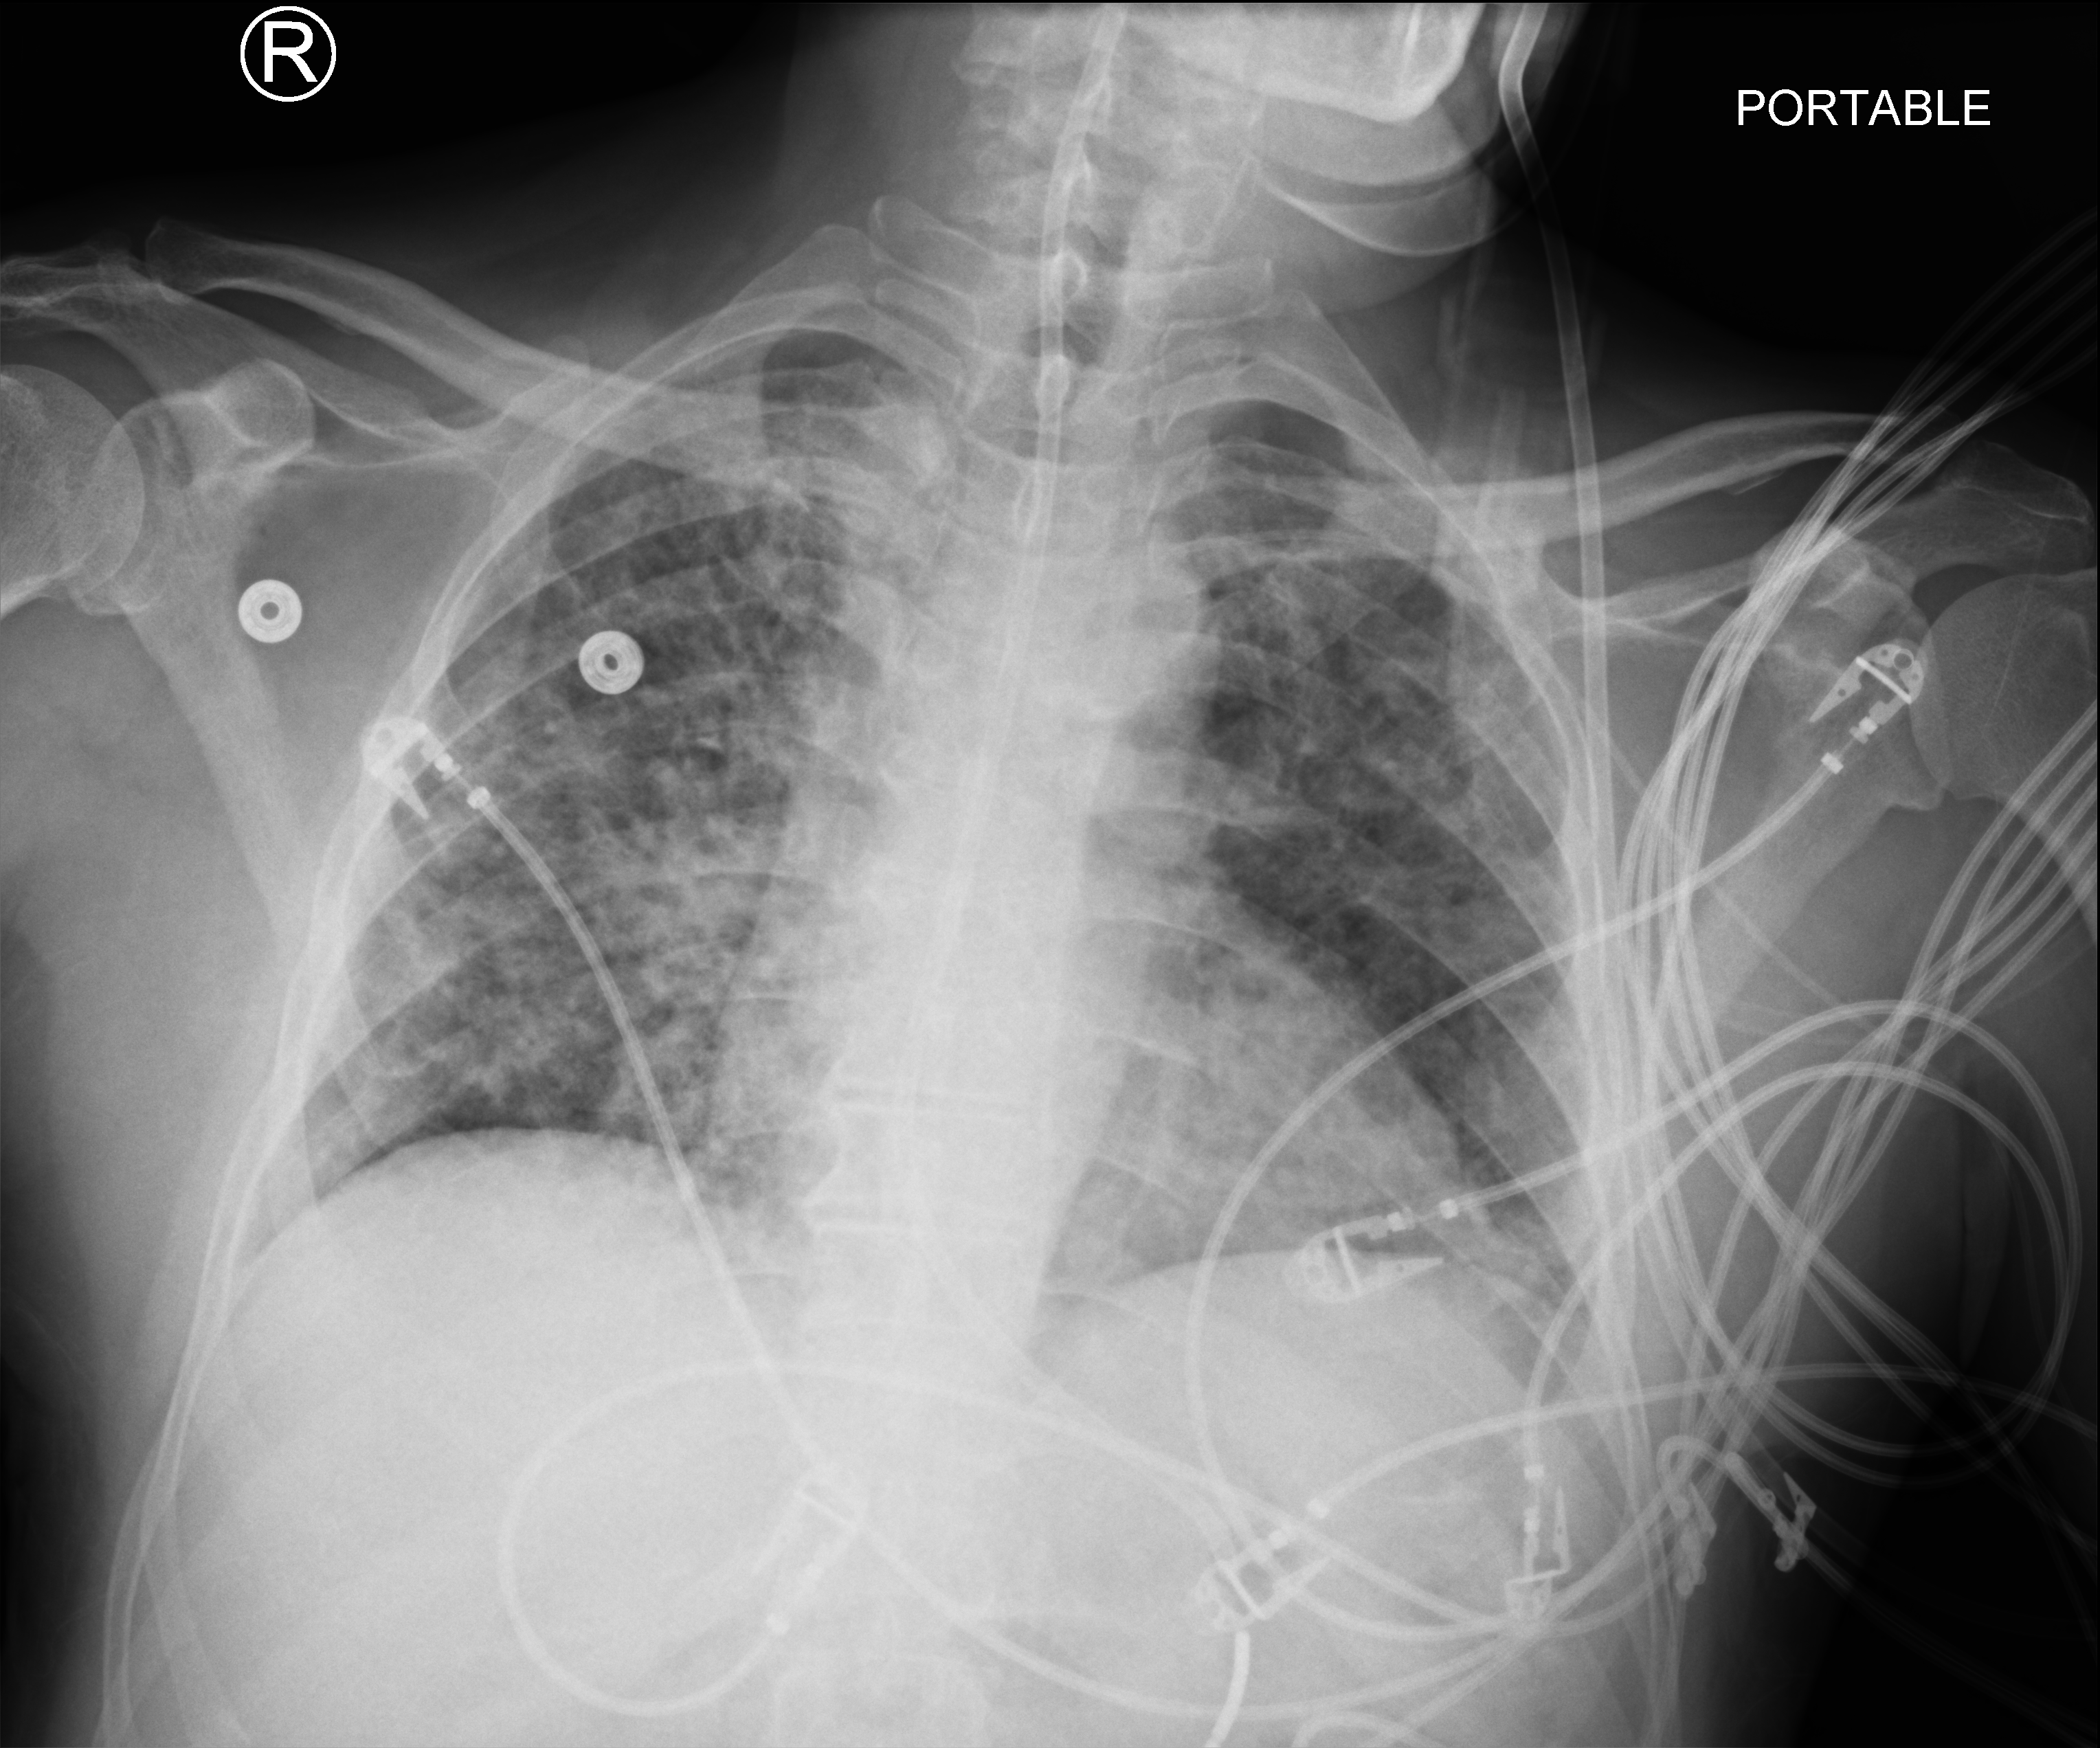
Portable chest radiograph; anteroposterior (AP) projection. Male patient hospitalised with COVID-19, age 18–59 years.
From the hospital-stay record, not from the radiograph (when in the stay this image was taken is not recorded):
- mechanically ventilated during this hospital stay: yes
- length of hospital stay: 32 days